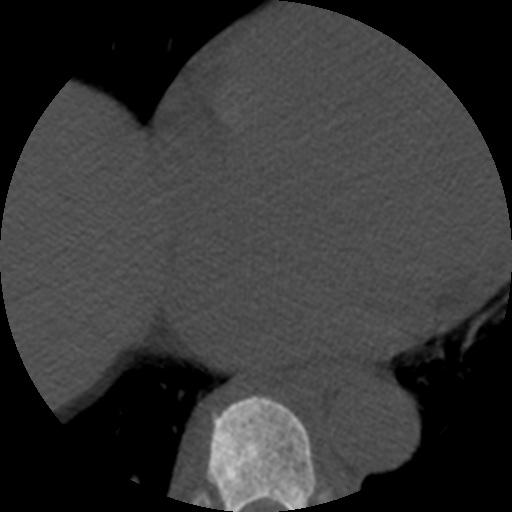
CT including the spine, one axial slice; slice 314 of 508 in the series (ordered by position); reconstruction kernel STANDARD; bone window (W 1800 / L 400 HU); 1.25 mm slice thickness; 512 × 512 image matrix. Patient age 57 years. From the clinical record (not read from this slice): primary cancer: prostate.
Annotated regions visible in this slice (semi-automatically segmented with operator editing):
- T8 vertebra: box from (x=207, y=395) to (x=317, y=512) px